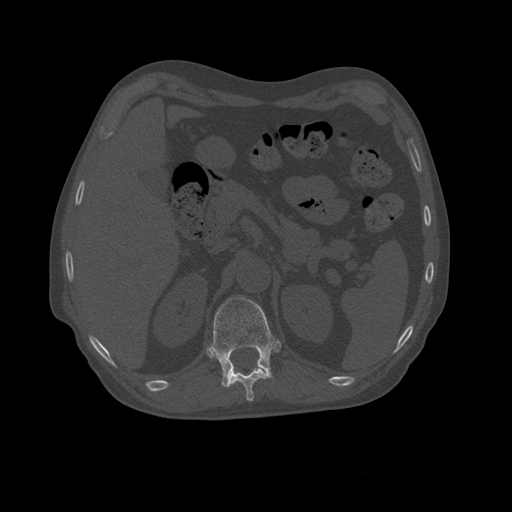
CT including the spine, one axial slice; slice 387 of 450 in the series (ordered by position); reconstruction kernel STANDARD; 120 kVp; bone window (W 1800 / L 400 HU); 1.25 mm slice thickness; 512 × 512 image matrix, field of view 405 × 405 mm. Patient age 75 years. From the clinical record (not read from this slice): primary cancer: prostate.
Structures marked on this image (semi-automatically segmented with operator editing):
- T10 vertebra: bounding box <211,348,275,402> (left, top, right, bottom; pixels)
- T11 vertebra: <210,296,276,388>